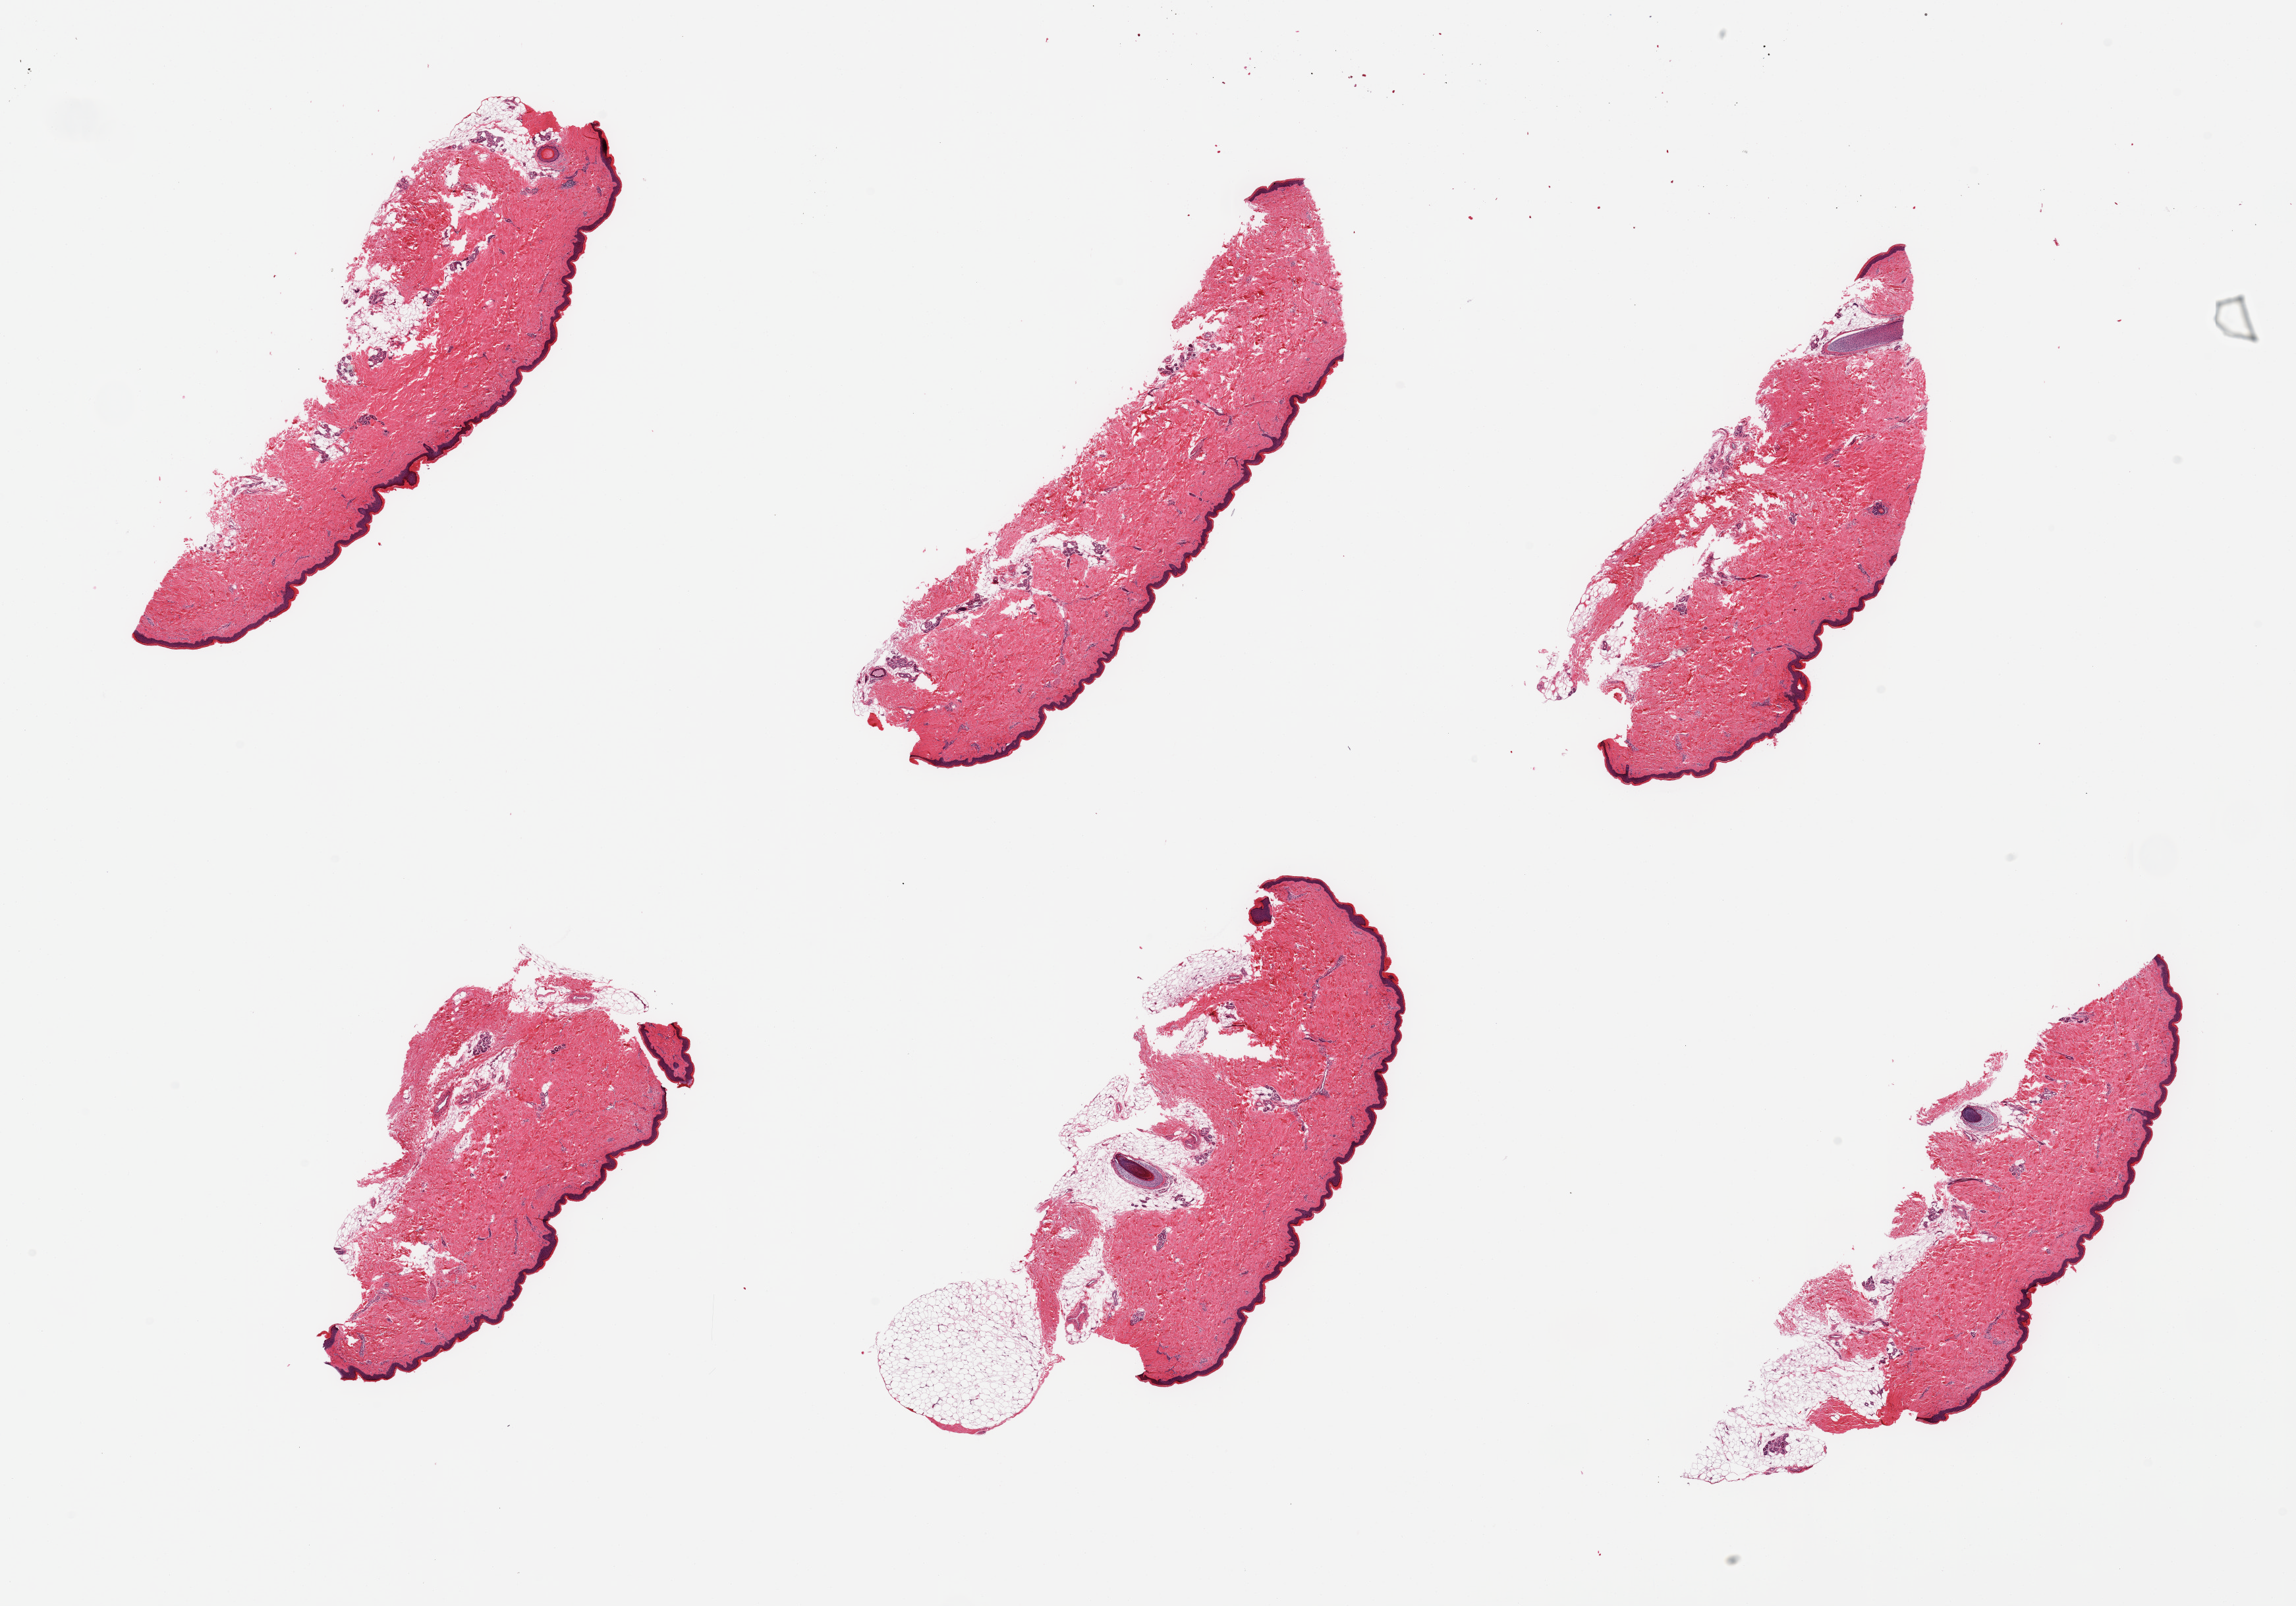
Whole-slide image, haematoxylin and eosin stain, brightfield, a low-resolution overview of the entire scanned area, about 27.6 x 19.3 mm; PAXgene-fixed, paraffin-embedded tissue; section of skin of lower leg (target tissue); tissue donor sample. Female donor.
Review note (as recorded): 6 pieces; from 5-25% fat (mostly attached), epidermis measures about 49 microns.